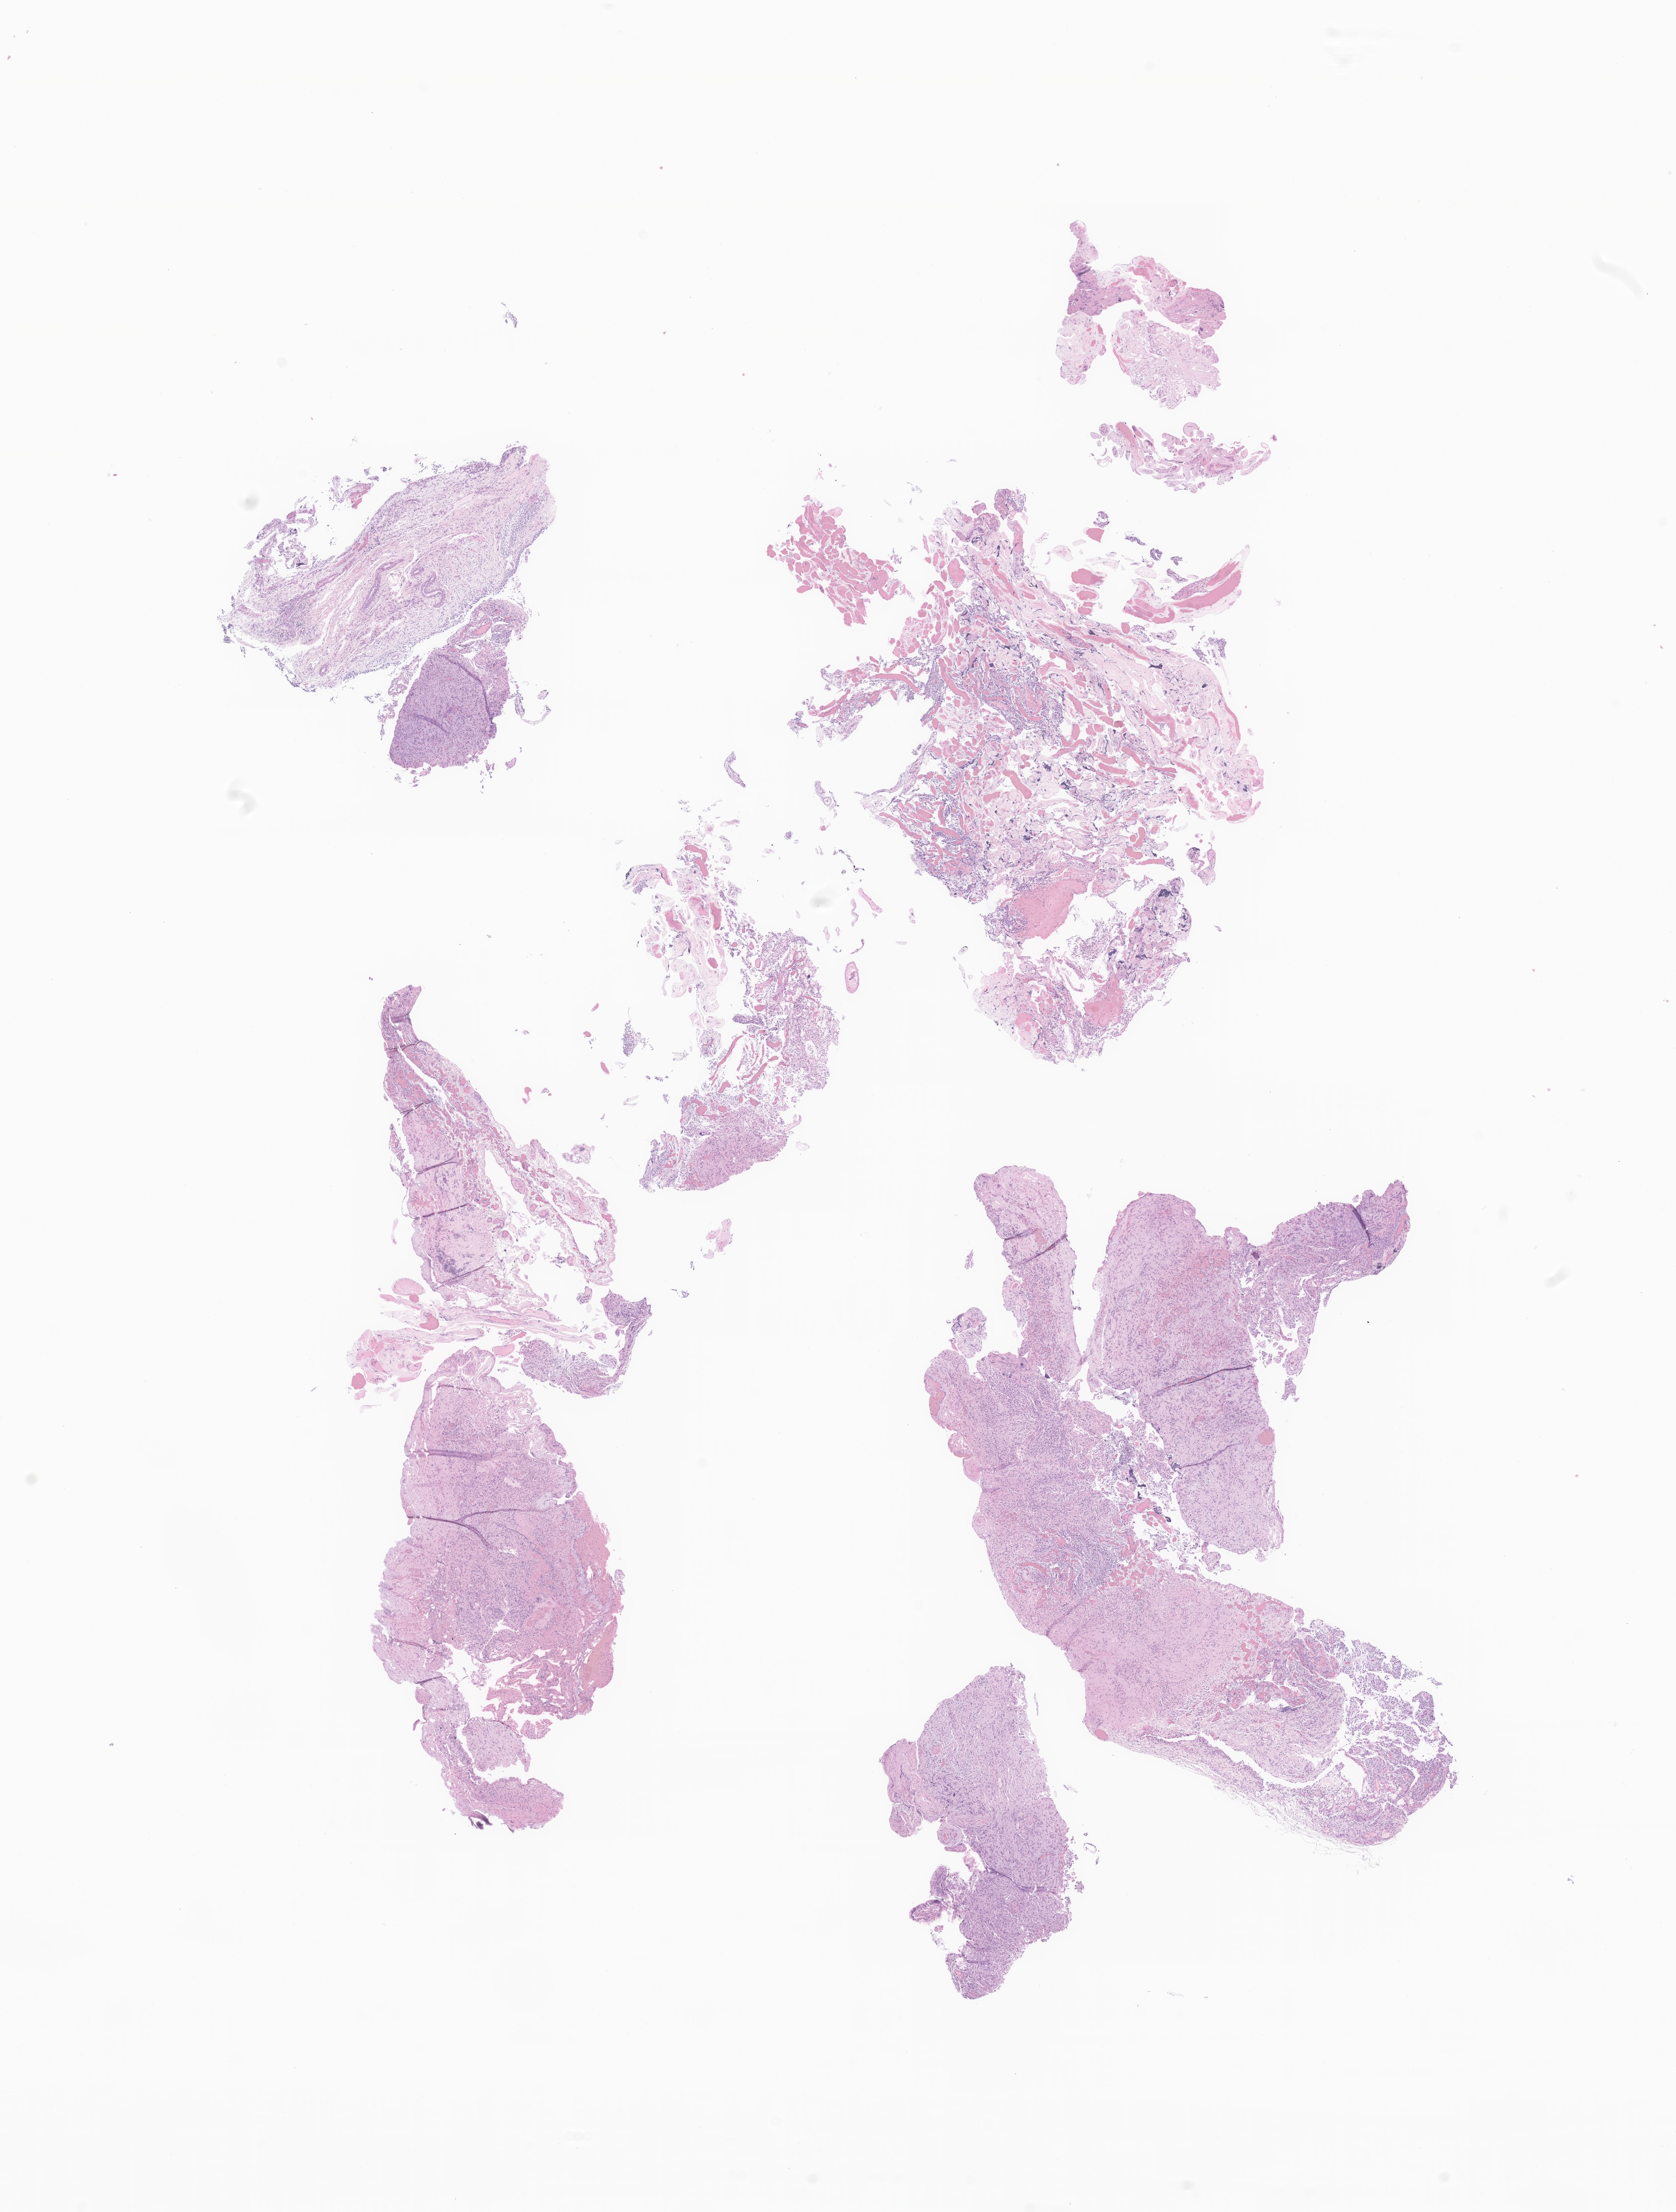
Digitized hematoxylin and eosin (H&E)-stained section of tumor tissue from the brain, low-resolution overview of the scanned area, about 14.2 x 18.8 mm; FFPE section. Patient female; age 97 months (8 years 1 month).
Recorded diagnosis: Pilocytic astrocytoma.